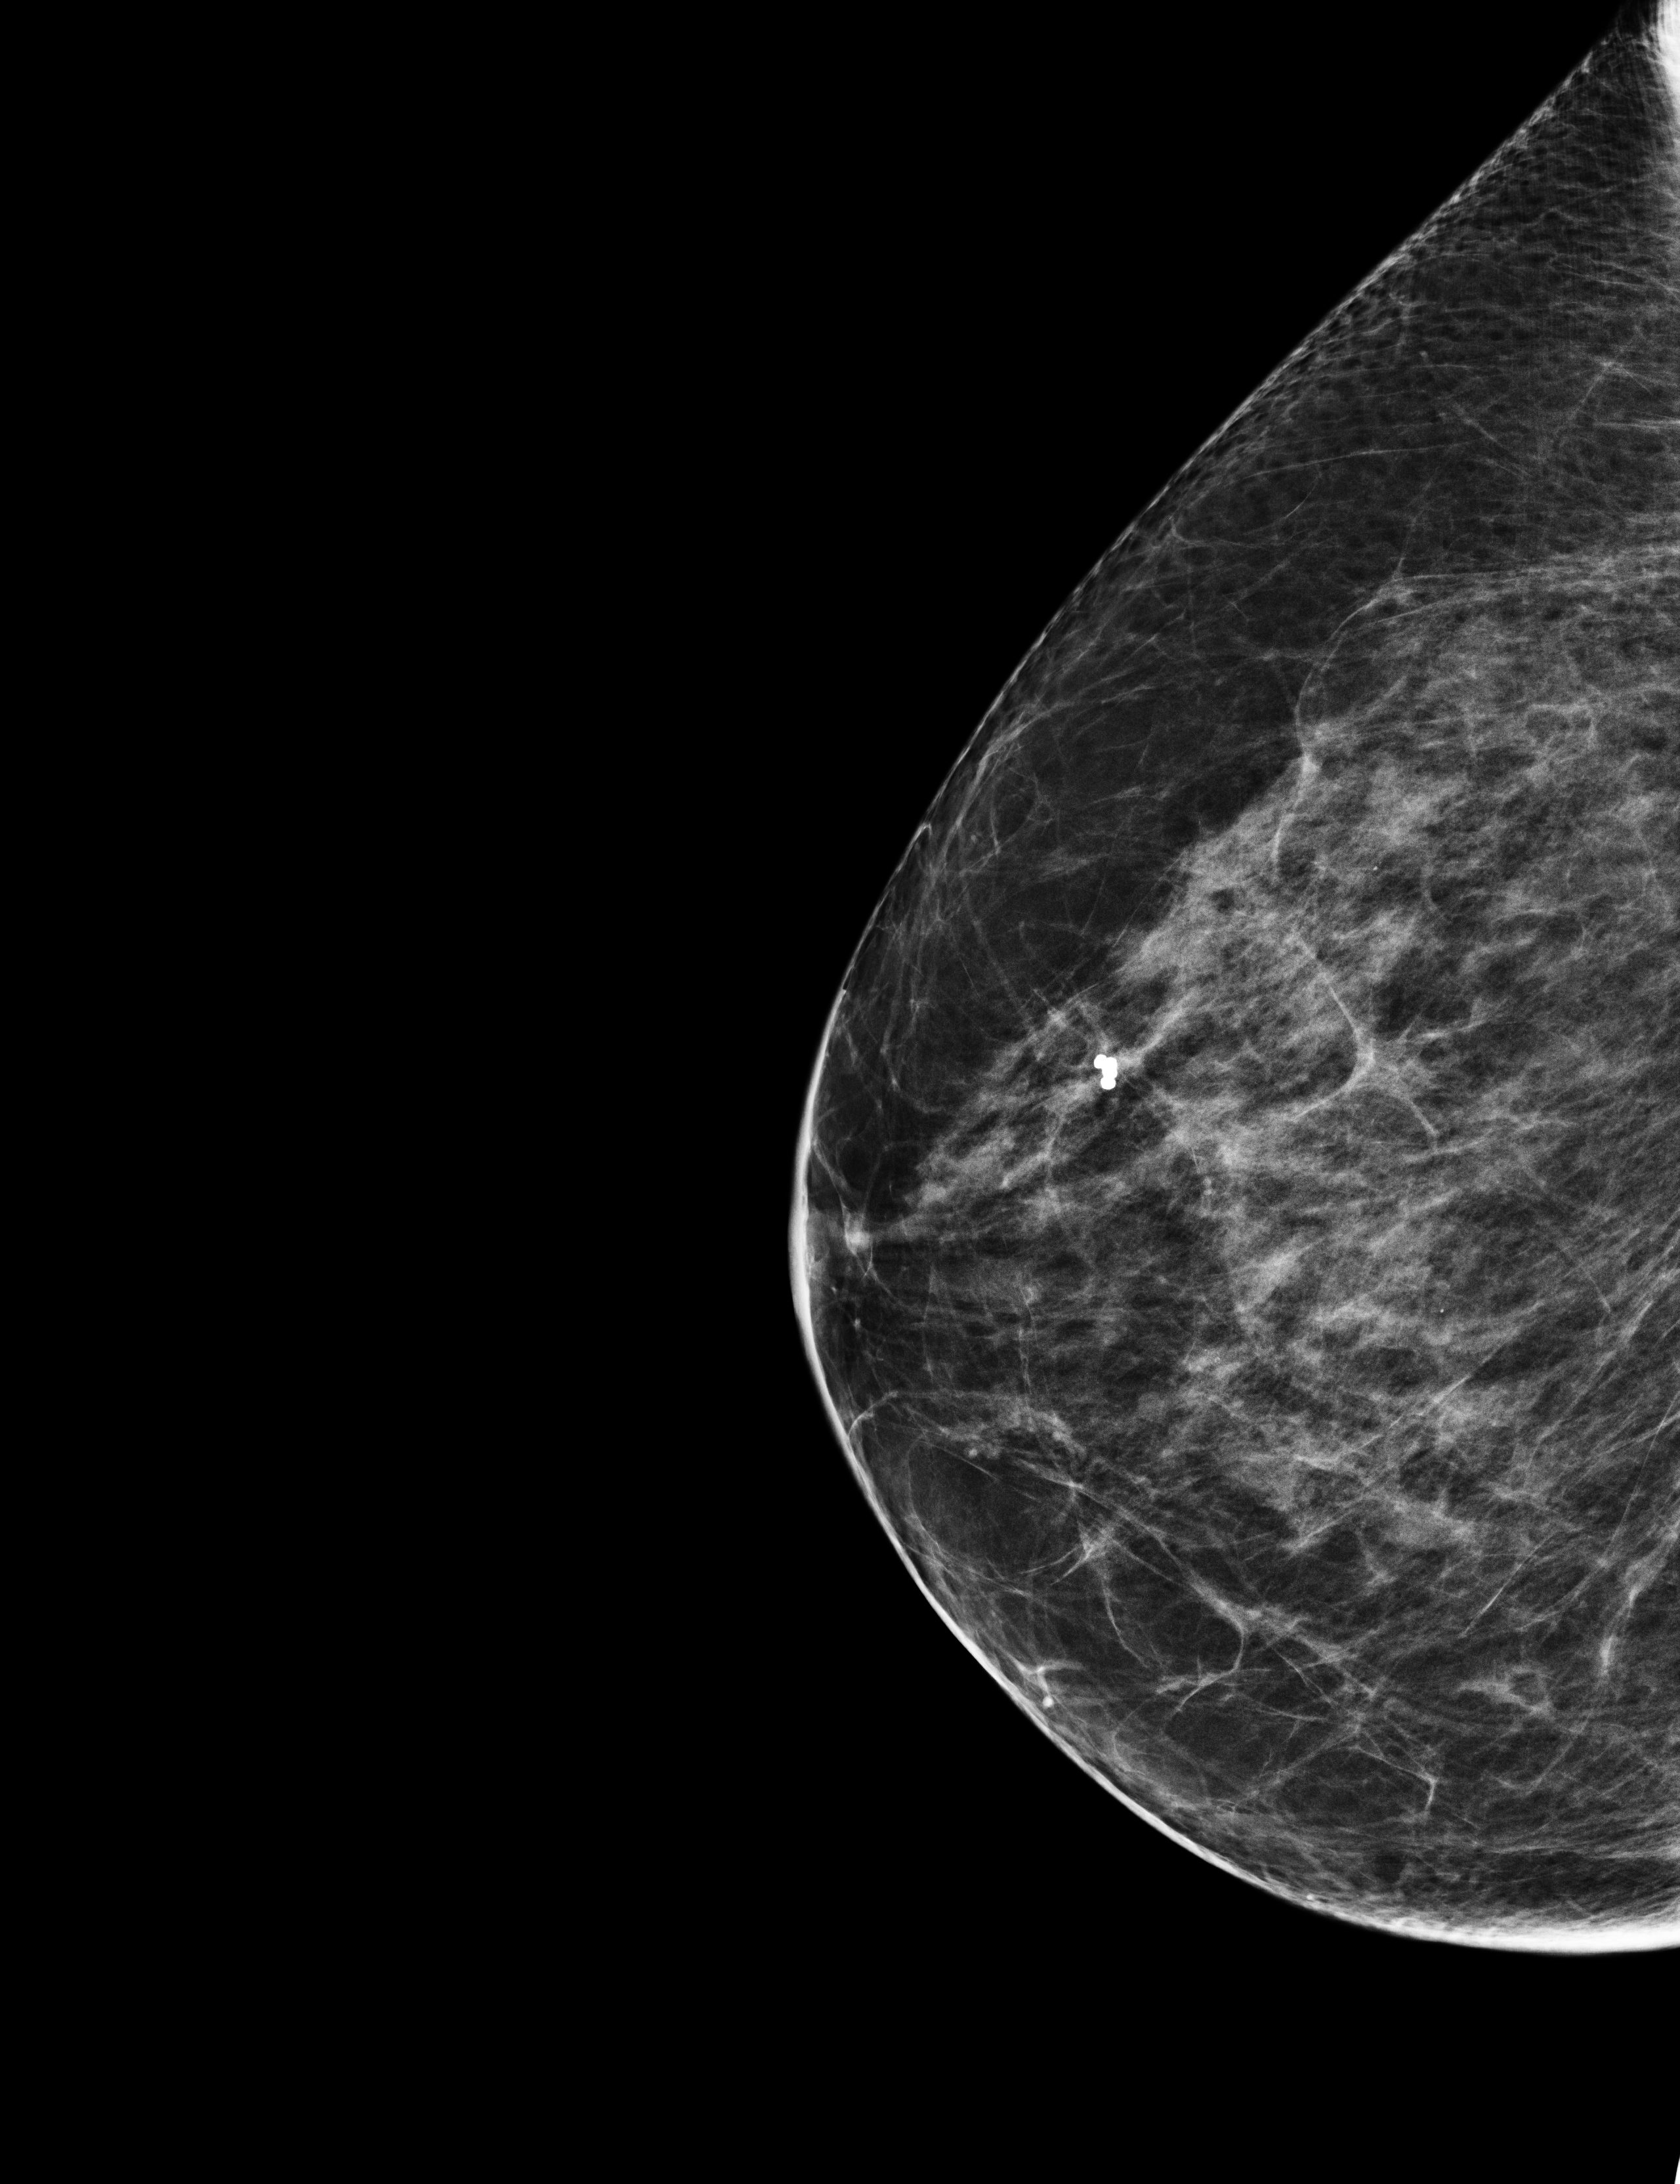
Full-field digital mammogram (FFDM), right breast, craniocaudal (CC) view, annual screening mammography examination. Female patient, age 67 years.
- BI-RADS breast density category at the screening exam (both breasts, scale 1–4): 3
- final BI-RADS assessment for this screening round (tomosynthesis exam, both breasts): category 2
- recall: no recall after this screen